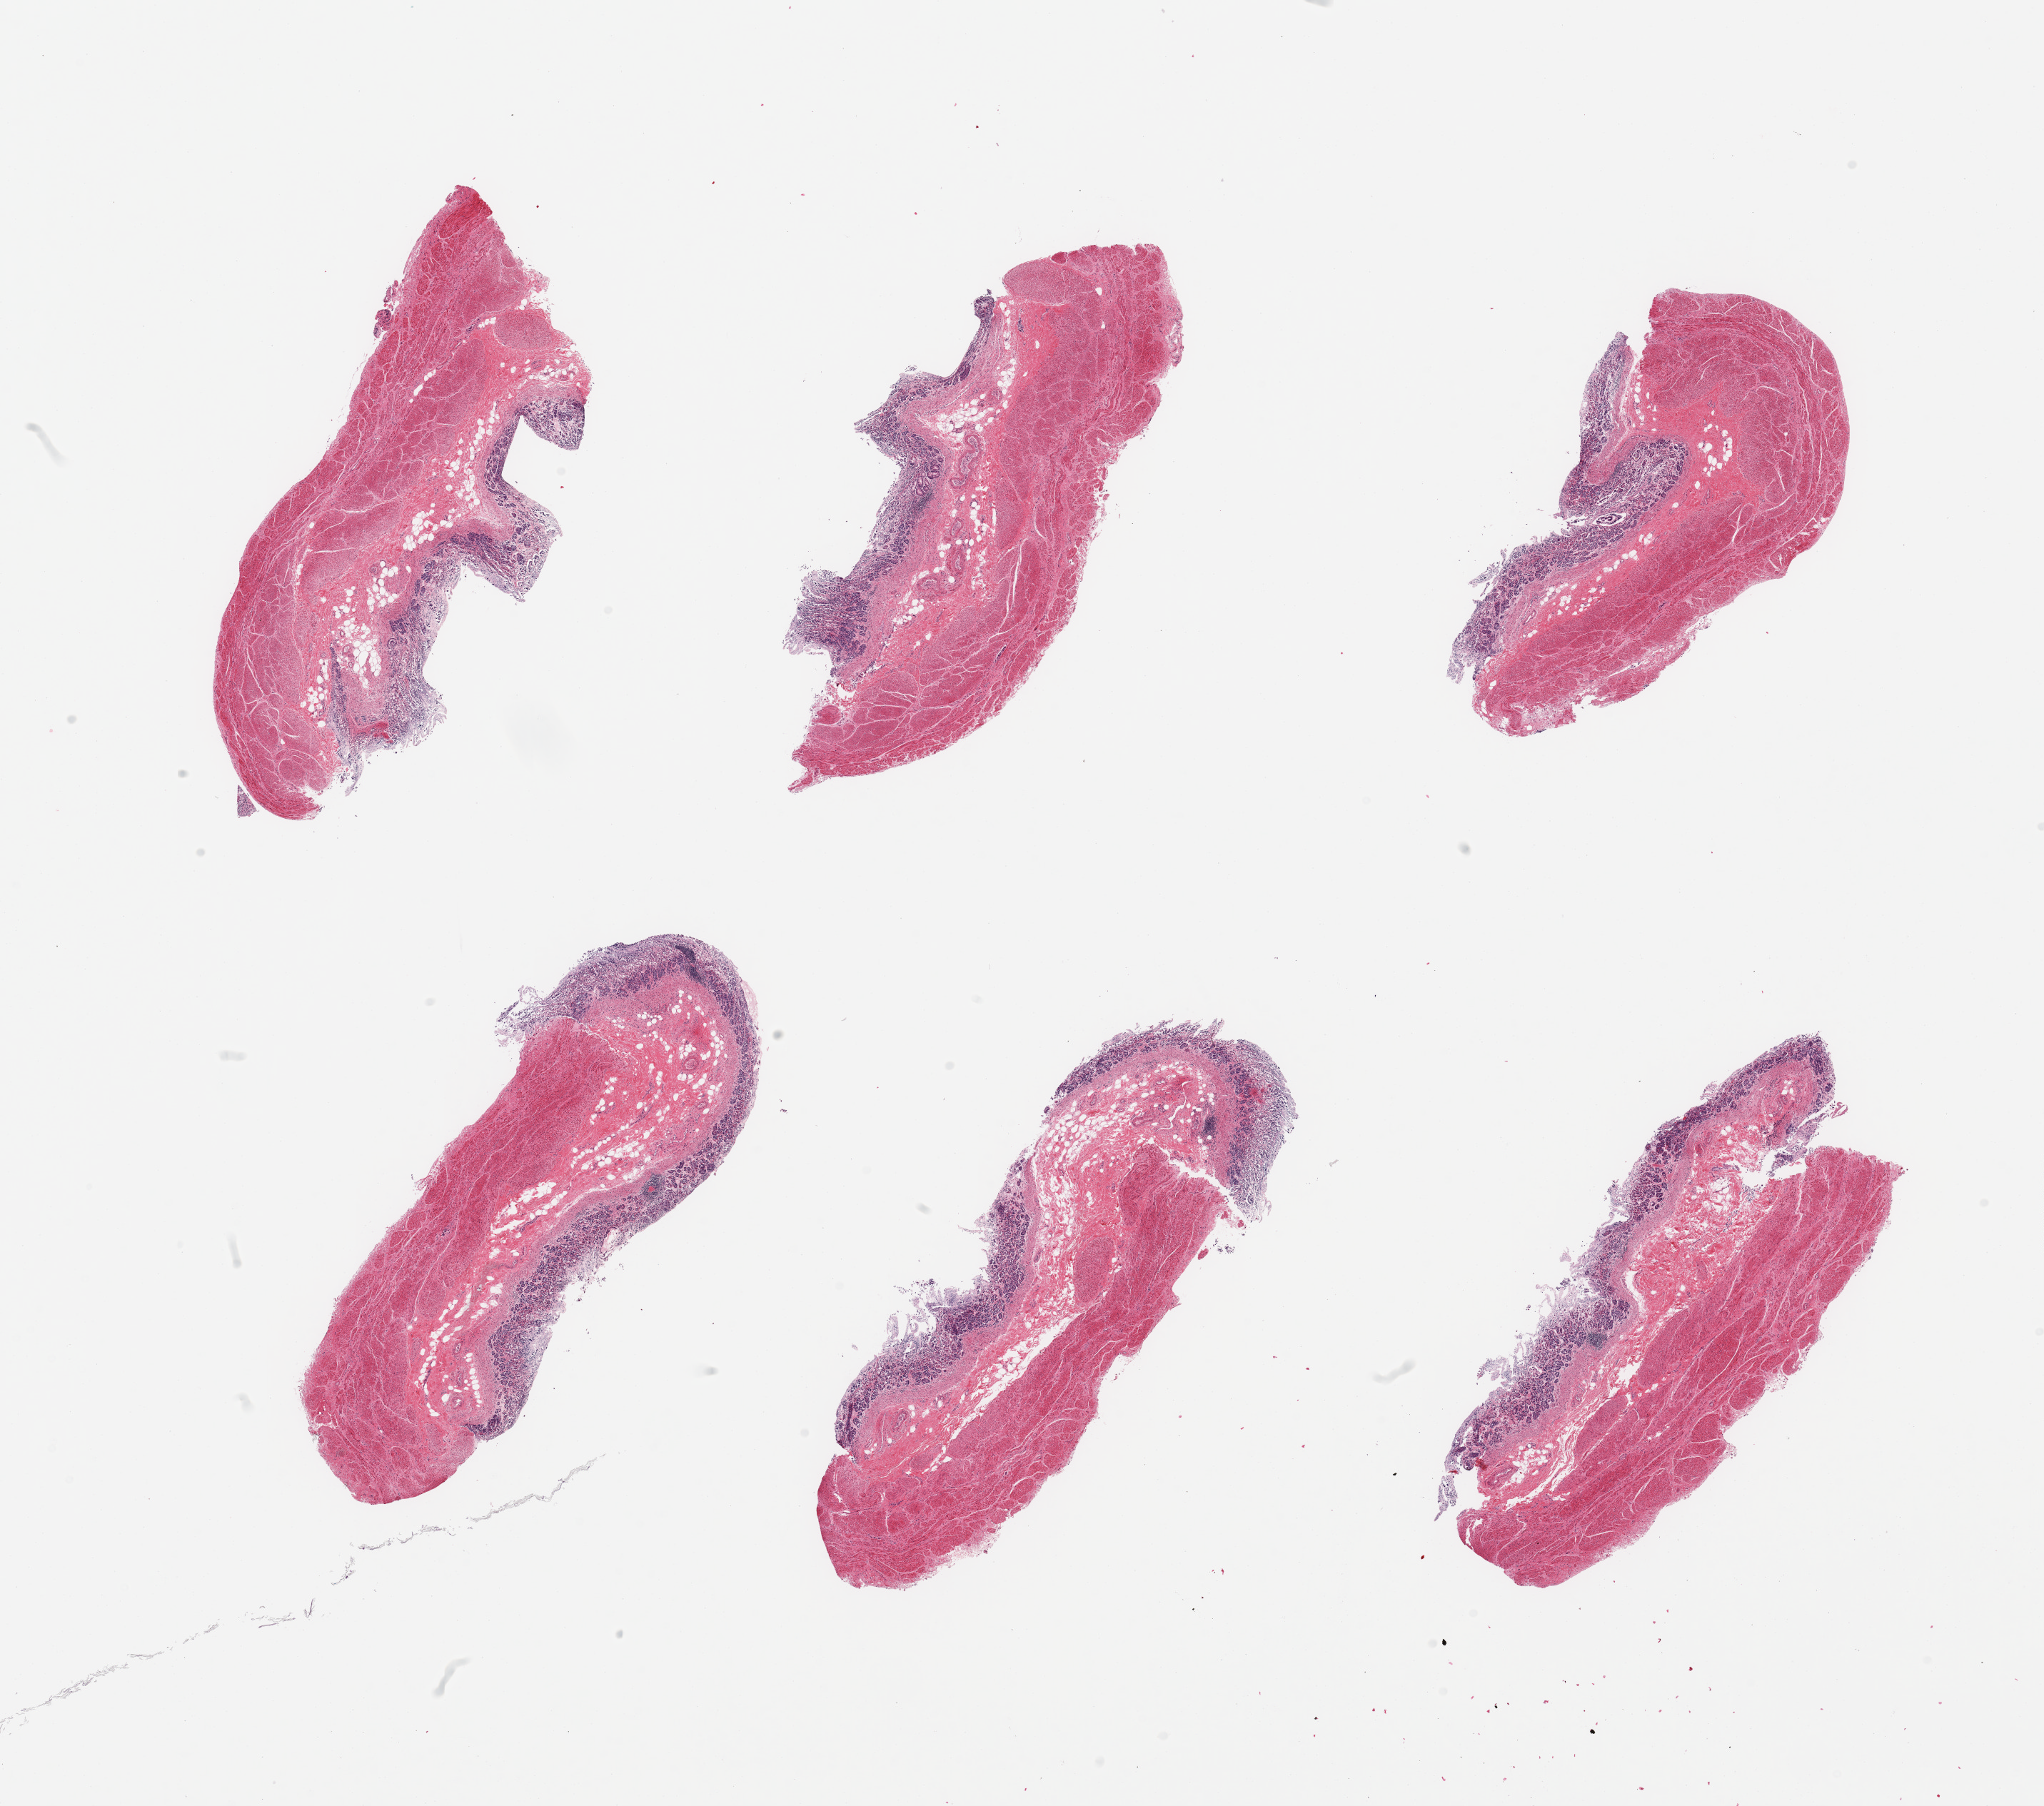
Whole-slide image, haematoxylin and eosin stain — a low-resolution overview of the entire scanned area, about 22.6 x 20.0 mm; PAXgene-fixed paraffin-embedded (PFPE) section; target tissue: stomach; donor tissue sample. Donor: male.
Pathologist's review note for this sample: 6 pieces, target mucosa up to ~0.7mm but with advanced autolysis.